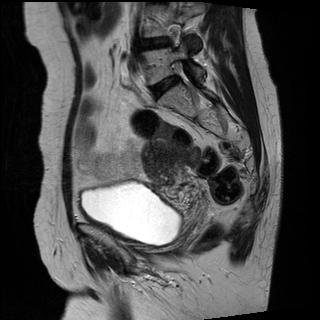
Pelvic MRI for cervical cancer, one sagittal slice. T2-weighted. 1.5 T. TE 89 ms, TR 2740 ms. 4 mm slice thickness. 320 × 320 image matrix, field of view 260 × 260 mm. Female patient, age 42 years.
Annotated regions visible in this slice (manually delineated by an expert):
- uterus and cervix: box from (x=142, y=140) to (x=184, y=181) px